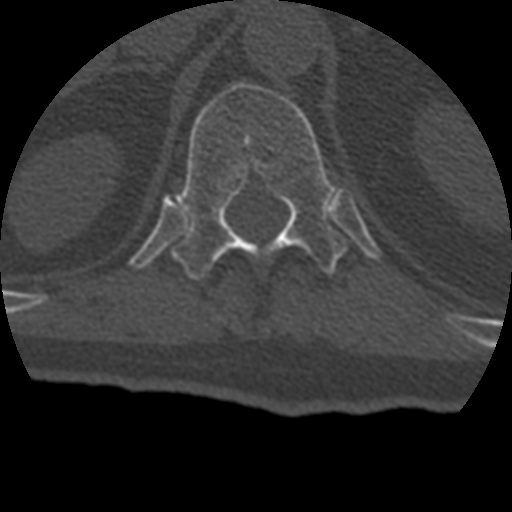
CT including the spine, one axial slice. Slice 176 of 399 in the series (ordered by position). Bone window (W 1800 / L 400 HU). 512 × 512 image matrix, field of view 160 × 160 mm. Patient age 69 years. From the clinical record (not read from this slice): primary cancer: prostate.
Annotated regions visible in this slice (semi-automatic segmentation, software-assisted and operator-edited):
- T12 vertebra: bounding box <171,82,348,280> (left, top, right, bottom; pixels)